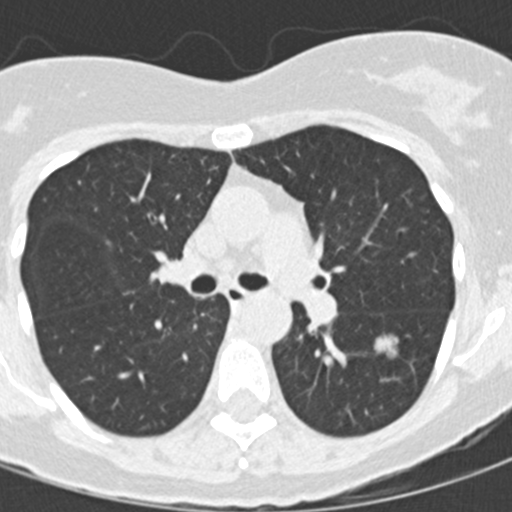
Low-dose screening chest CT, one axial slice; slice 90 of 145 in the series (ordered by position); reconstruction kernel B30f; lung window (W 1500 / L -600 HU); 2 mm slice thickness; 512 × 512 image matrix.
Outlined on this slice (expert manual segmentation):
- lesion 1 (tumor, lower lobe of left lung): box from (x=375, y=335) to (x=398, y=357) px